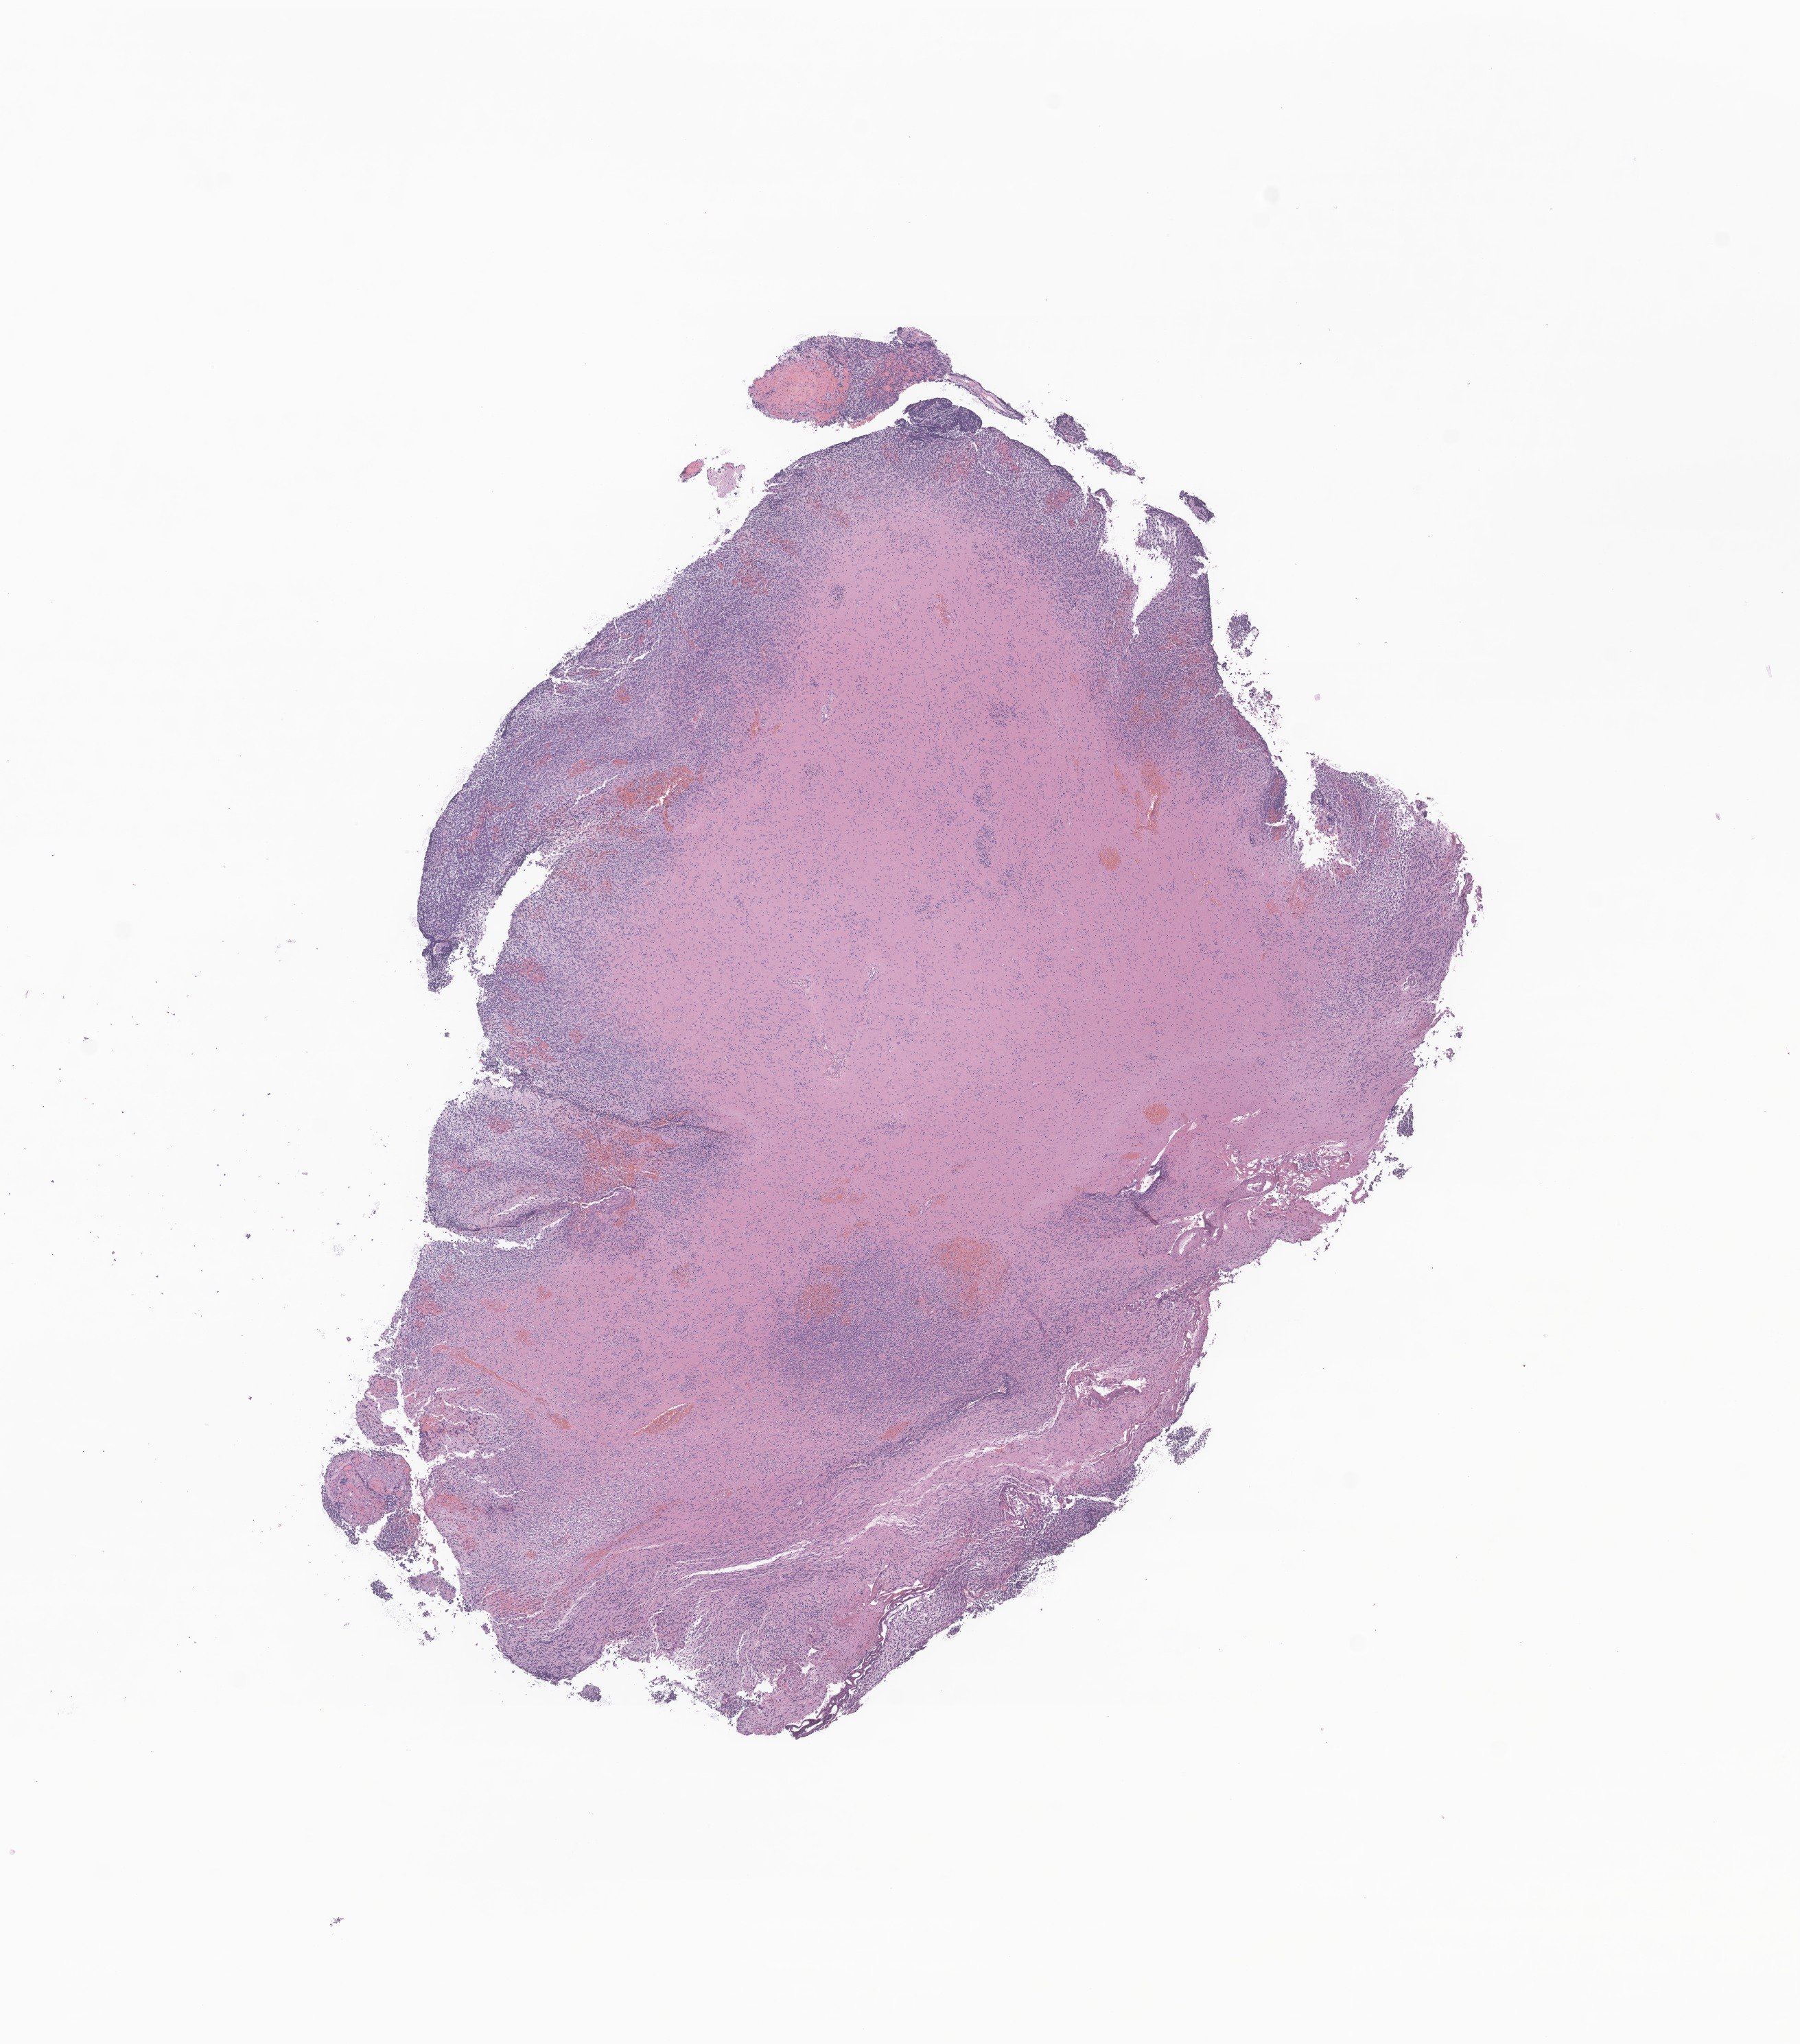
Whole-slide image, hematoxylin and eosin (H&E) stain of tumor tissue from the brain — shown as a low-resolution overview of the whole scanned area (about 11.1 x 12.6 mm); FFPE section. Patient female; age 108 months (9 years).
Recorded diagnosis: Neoplasm, uncertain whether benign or malignant.